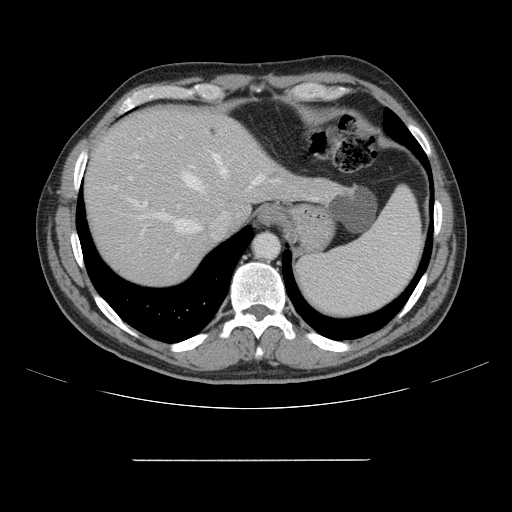
Contrast-enhanced abdominal CT, one axial slice. Slice 126 of 164 in the series (ordered by position). 120 kVp. Intravenous contrast given. Soft-tissue window (W 400 / L 40 HU). 2.5 mm slice thickness. 512 × 512 image matrix, field of view 404 × 404 mm. Male patient, age 54 years. Case-level facts recorded for this patient, not image findings: diagnosis: colorectal cancer liver metastases, imaged before liver resection; multiple liver metastases: yes; largest metastasis: 1 cm; disease in both lobes: no.
Structures marked on this image (outlined manually by an expert reader):
- hepatic veins: box from (x=137, y=154) to (x=265, y=232) px
- liver: (x=86, y=108)–(x=336, y=285)
- planned liver remnant (the part of the liver to remain after resection): (x=86, y=108)–(x=256, y=284)
- portal vein (with intrahepatic branches): (x=129, y=136)–(x=214, y=234)
- liver metastasis: (x=269, y=173)–(x=279, y=180)